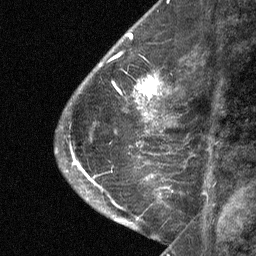
Breast MRI (dynamic contrast-enhanced), one sagittal slice; slice 22 of 64 in the series (ordered by position); dynamic contrast-enhanced study with each time point stored as its own series, time point 2 of 3 at this slice position (early post-contrast, ordered by acquisition time); 1.5 T; TE 4.8 ms, TR 27 ms; 256 × 256 image matrix, field of view 180 × 180 mm. Female patient, age 59 years. Case-level facts recorded for this patient, not image findings: setting: breast cancer imaged before/during neoadjuvant chemotherapy; receptor status: triple-negative.
Structures marked on this image (semi-automatic segmentation, software-assisted and operator-edited):
- analysis volume of interest (the breast-tissue region the enhancement analysis was run in; not a lesion): bounding box [x1, y1, x2, y2] px = [122, 58, 176, 109]
- tumour enhancement mask (voxels above the 90 % enhancement threshold inside the analysis volume of interest): [136, 74, 161, 102]